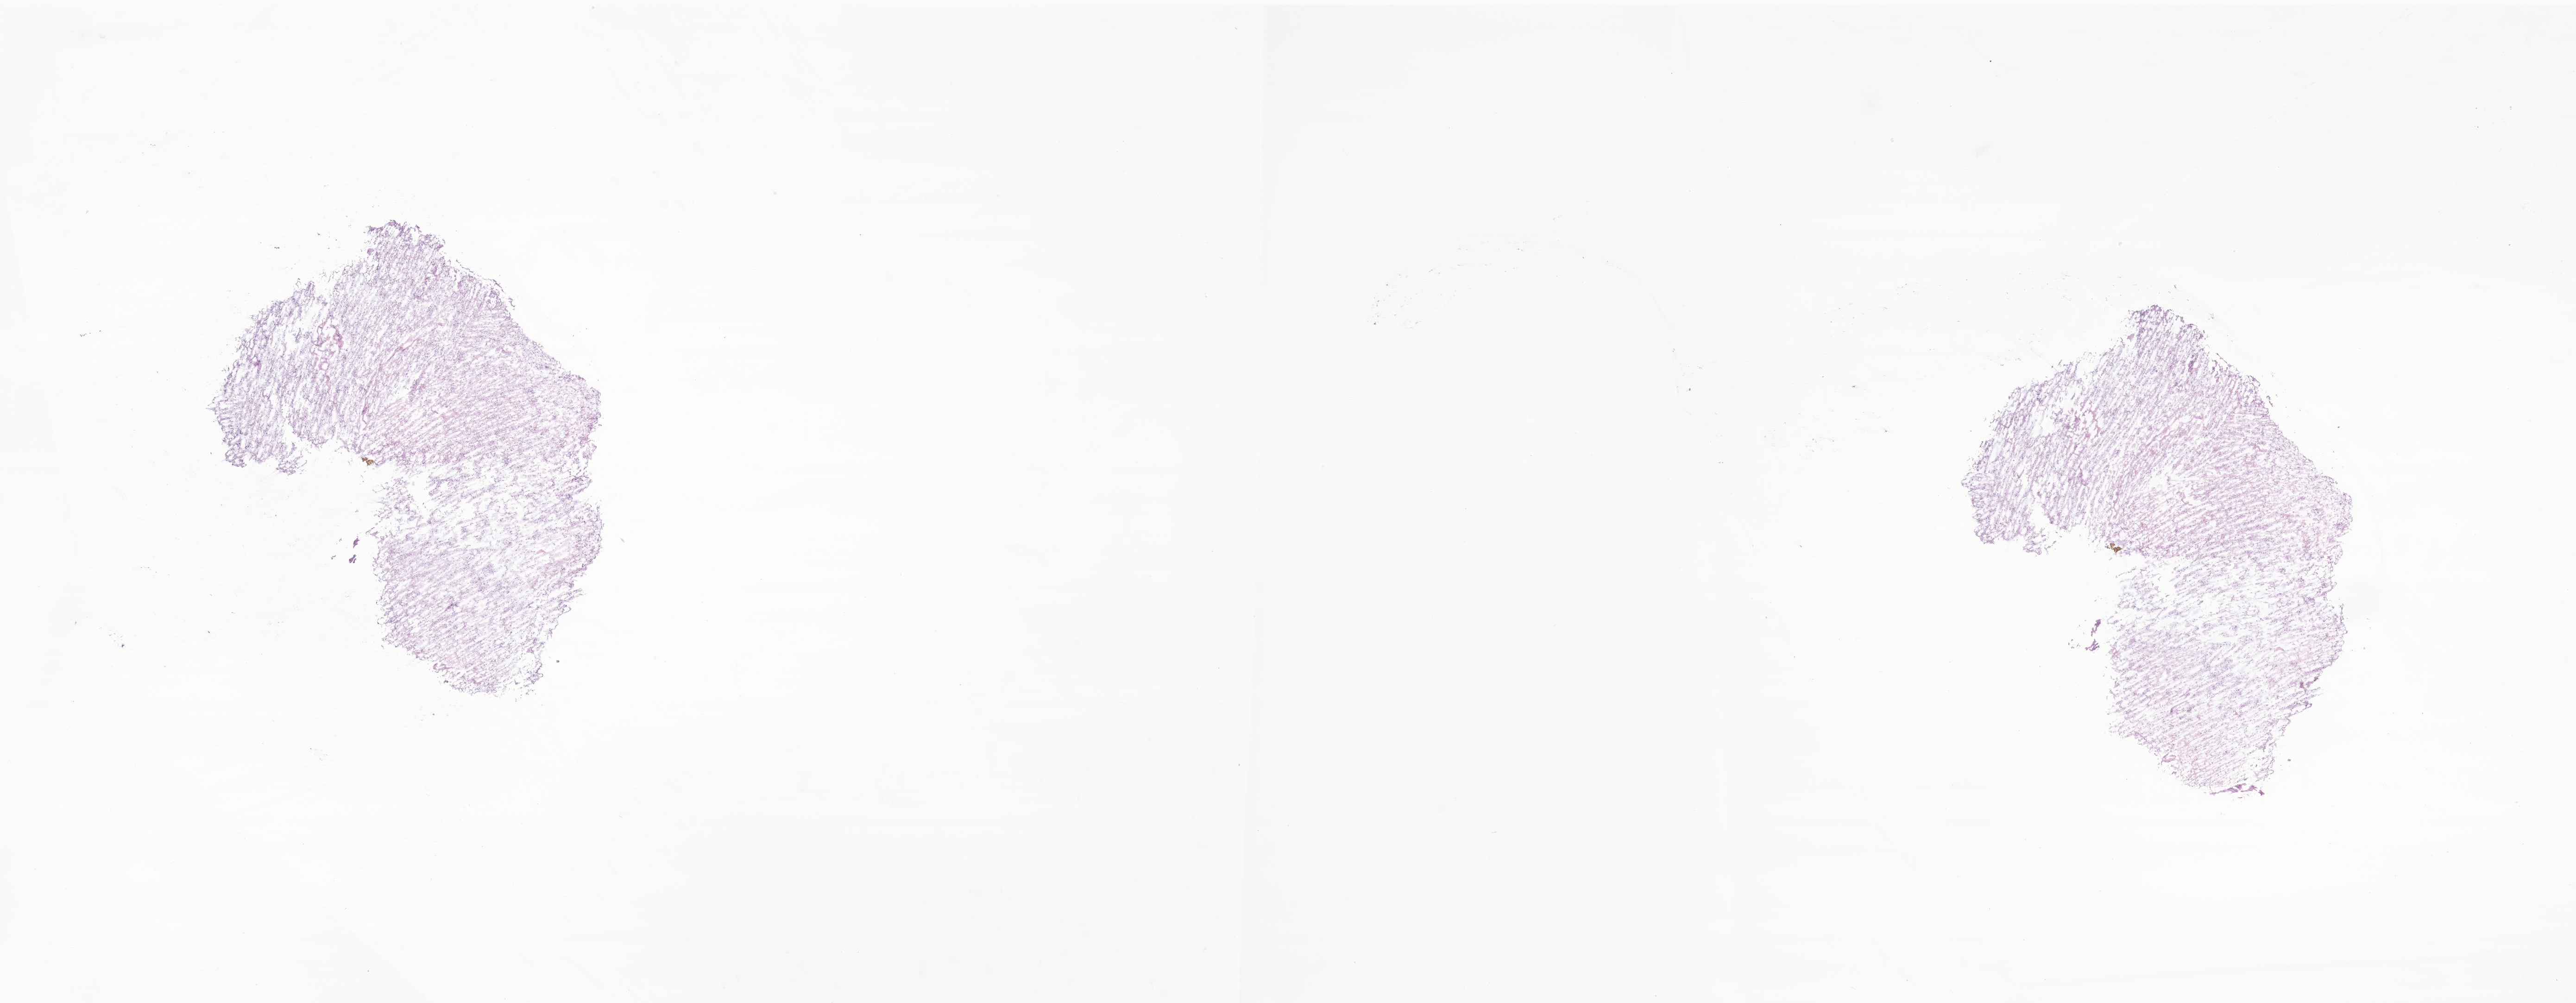
Hematoxylin and eosin (H&E) whole-slide image of tumor tissue from the spinal cord — a low-resolution overview of the entire scanned area, about 23.4 x 9.1 mm. Frozen section. Male patient, age 51 months (4 years 3 months).
Diagnosis (ICD-O-3 morphology term): Neoplasm, uncertain whether benign or malignant.